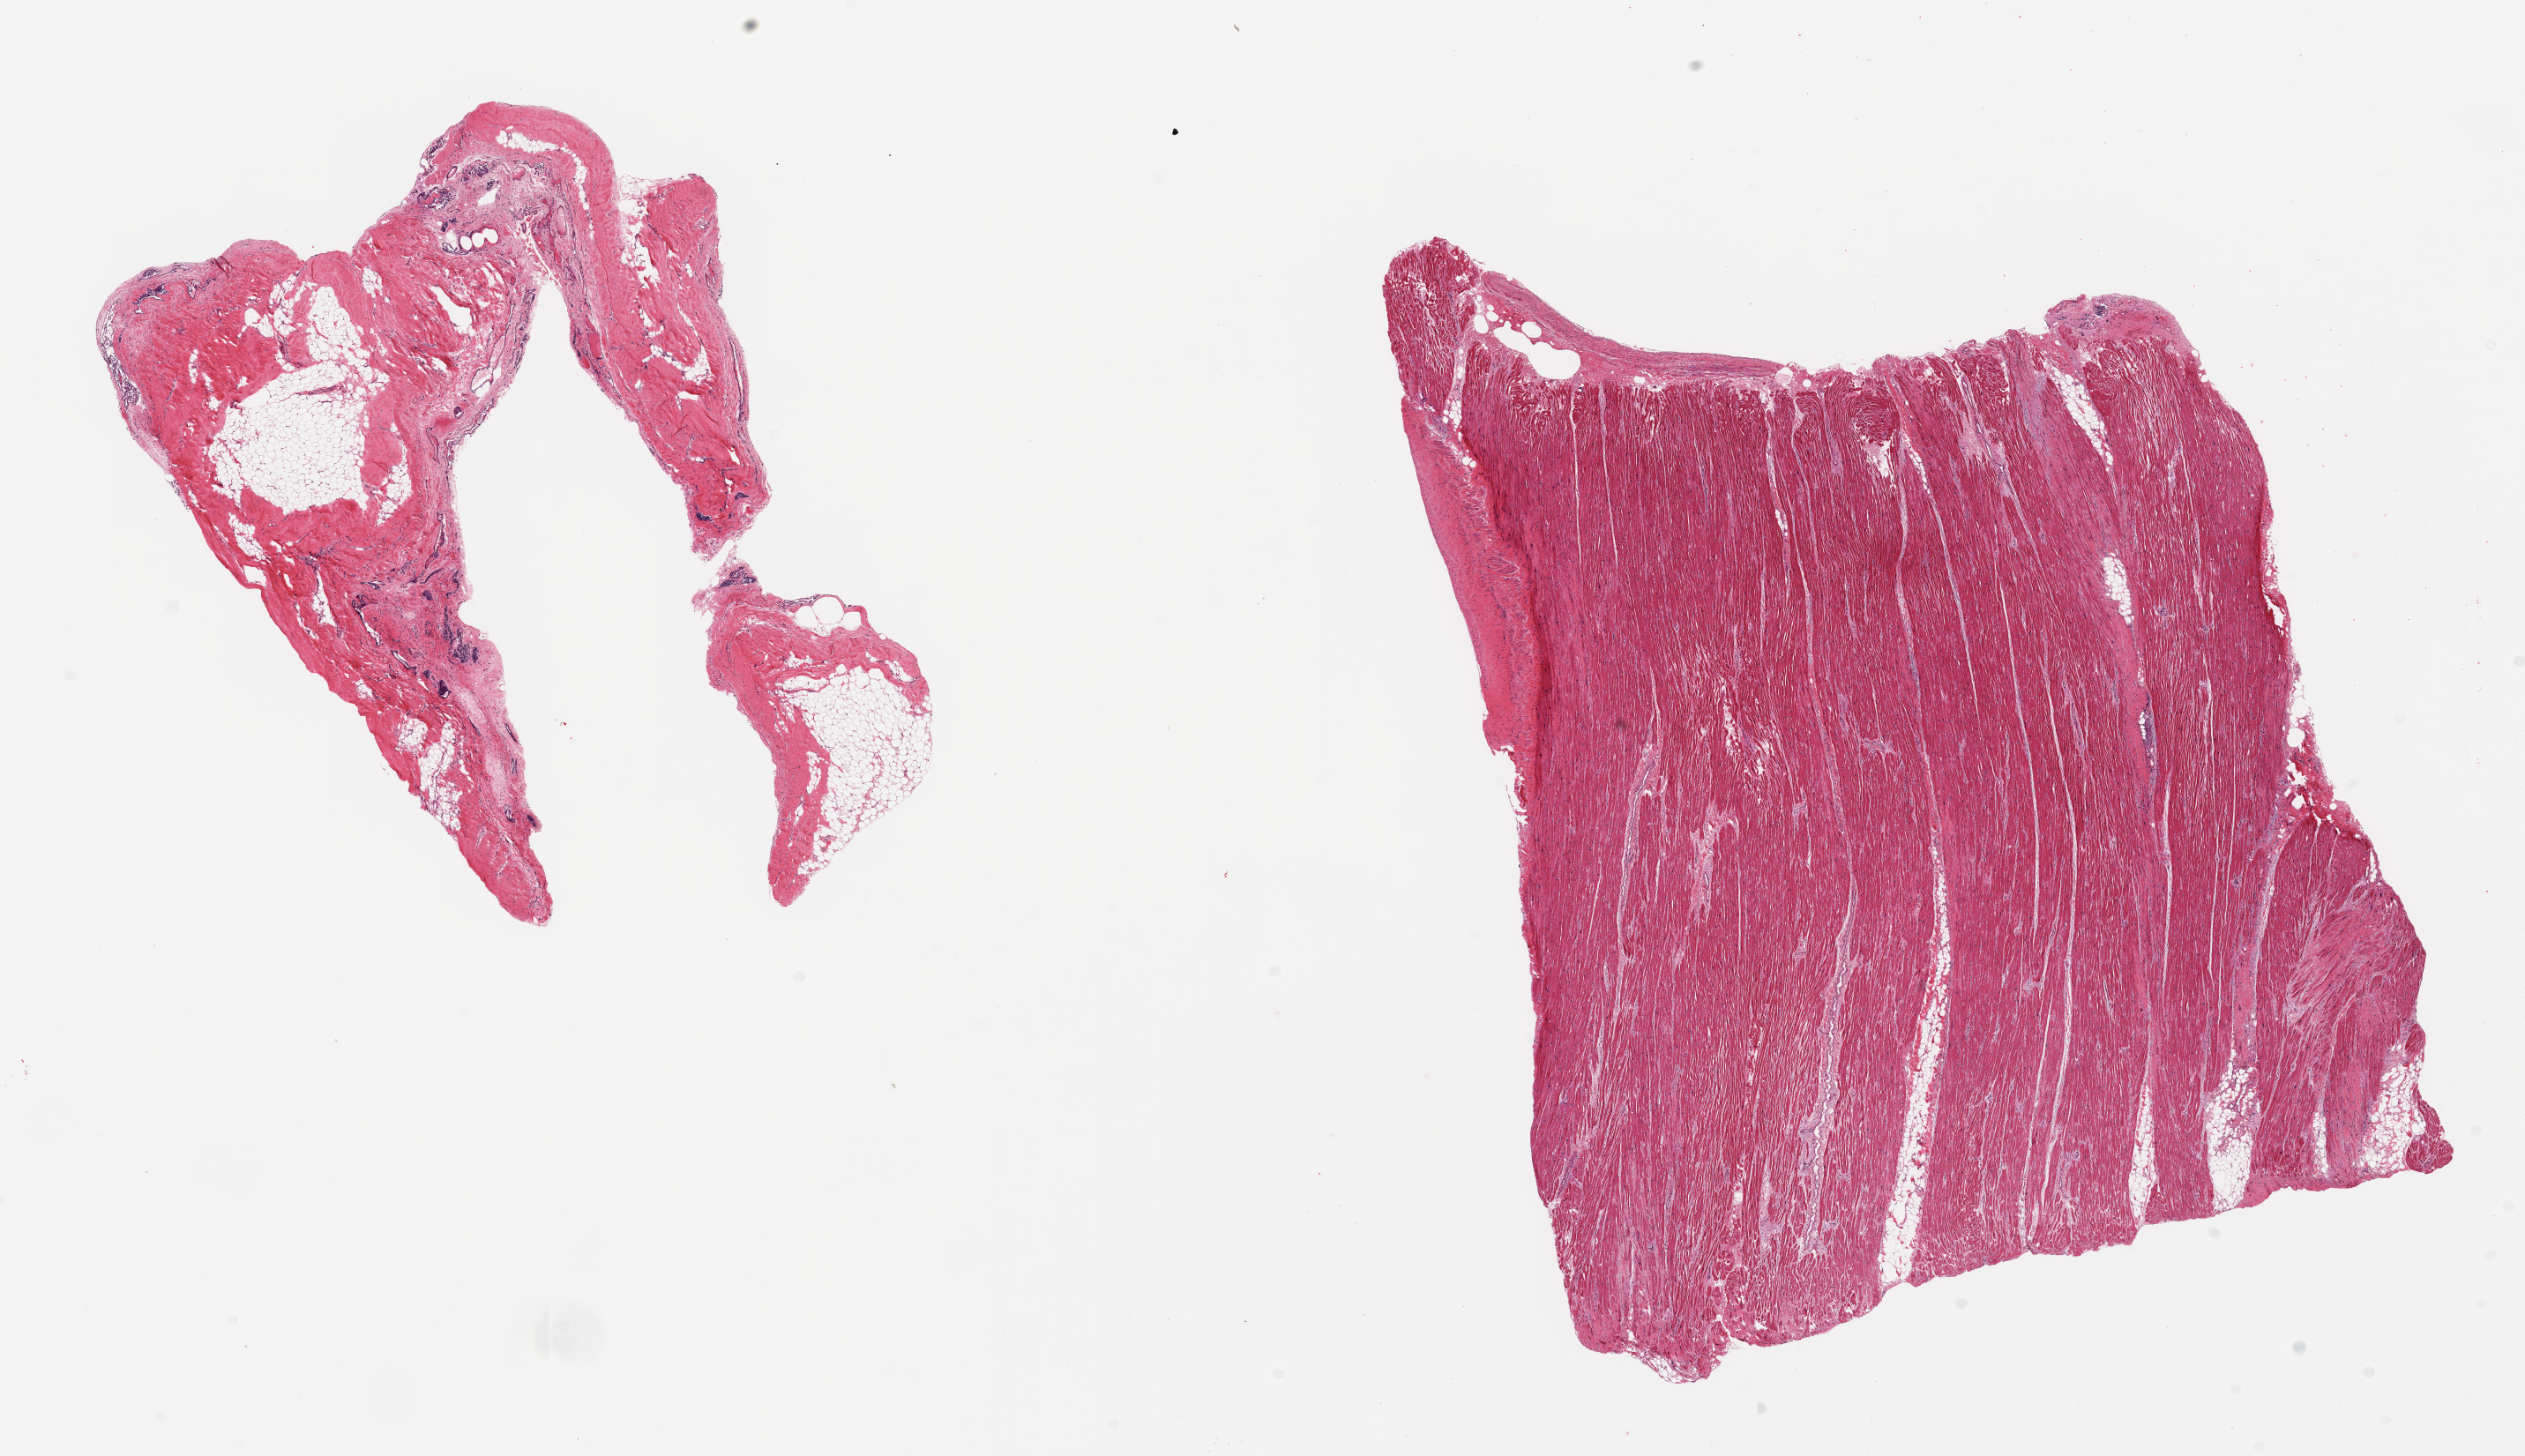
Hematoxylin and eosin (H&E) whole-slide image — shown as a low-resolution overview of the whole scanned area (about 22.6 x 13.1 mm), PAXgene-fixed, paraffin-embedded tissue, target tissue: auricular appendage, tissue donor sample. Donor: male.
* reviewer comment on this tissue sample: 2 pieces; smaller piece is all fibrofatty tissue; larger piece has 5% fibrofatty content